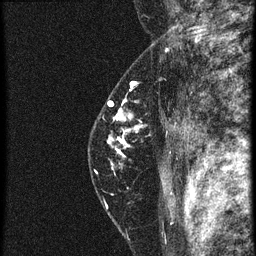
Breast MRI (dynamic contrast-enhanced), one sagittal slice; slice 44 of 60 in the series (ordered by position); 4 images stored at this slice position (order not interpretable as contrast timing); 1.5 T; TE 4.2 ms, TR 20.4 ms; 1.5 mm slice thickness; 256 × 256 image matrix, field of view 180 × 180 mm. Female patient, age 46 years. Case-level facts recorded for this patient, not image findings: setting: breast cancer imaged before/during neoadjuvant chemotherapy; receptor status: triple-negative.
Annotated regions visible in this slice (semi-automatically segmented with operator editing):
- analysis volume of interest (the breast-tissue region the enhancement analysis was run in; not a lesion): bounding box (x1, y1, x2, y2) in pixels: (88, 82, 181, 185)
- tumour enhancement mask (voxels above the 90 % enhancement threshold inside the analysis volume of interest): (108, 82, 143, 171)